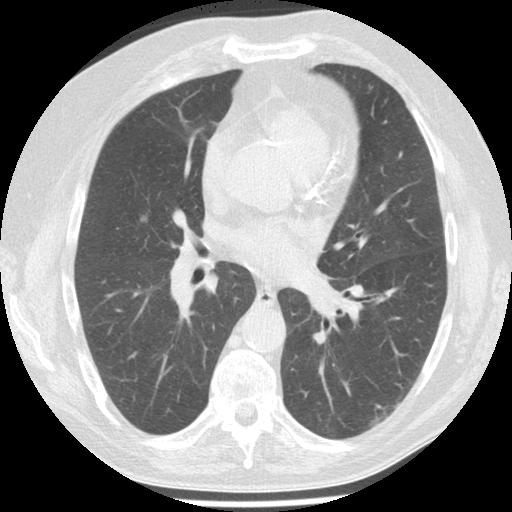
Low-dose screening chest CT, one axial slice; position 74 of 149 along the scan axis; reconstruction kernel STANDARD; 120 kVp; lung window (W 1500 / L -600 HU); 512 × 512 image matrix, field of view 340 × 340 mm.
Structures marked on this image (manually delineated by an expert):
- lesion 1 (tumor, middle lobe of right lung): bounding box (x1, y1, x2, y2) in pixels: (141, 217, 147, 221)